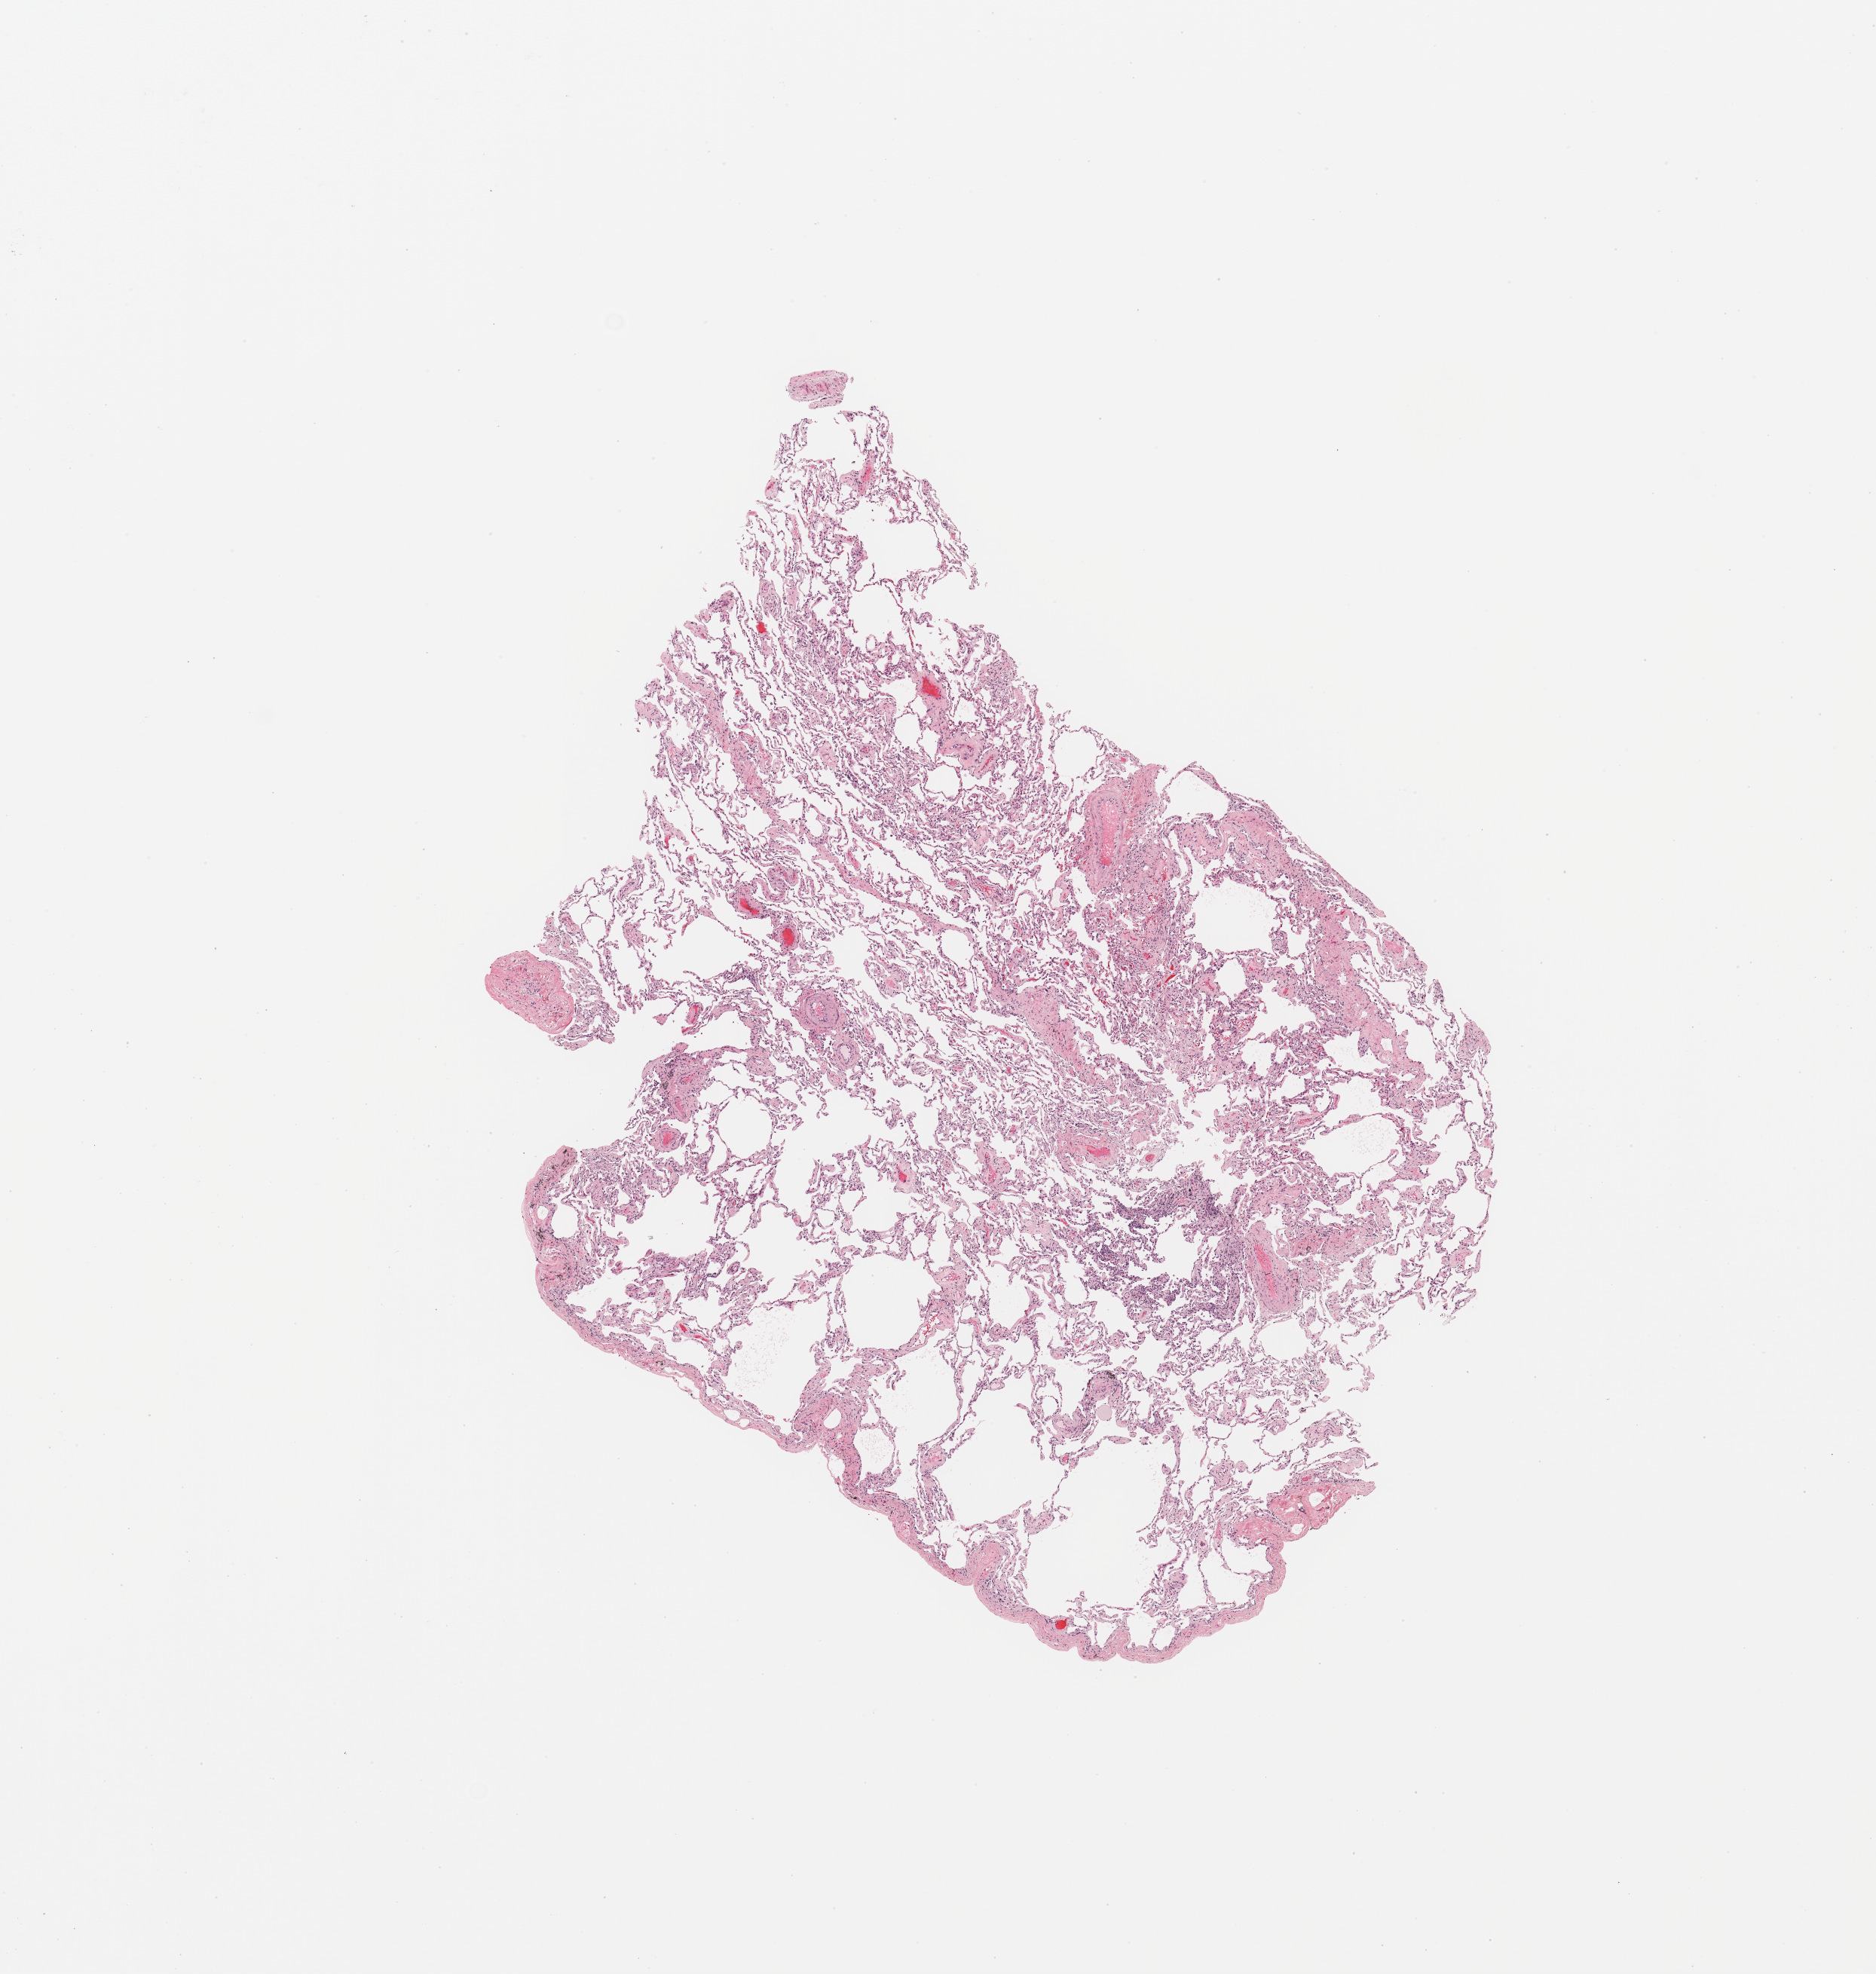
H&E-stained whole-slide image, low-resolution overview of the scanned area, about 9.8 x 10.4 mm, normal (non-tumour) tissue sample, sampled site: lung. Female, 65 y/o.
• this section: normal (non-tumour) tissue from the same patient
• patient diagnosis: Adenocarcinoma, NOS